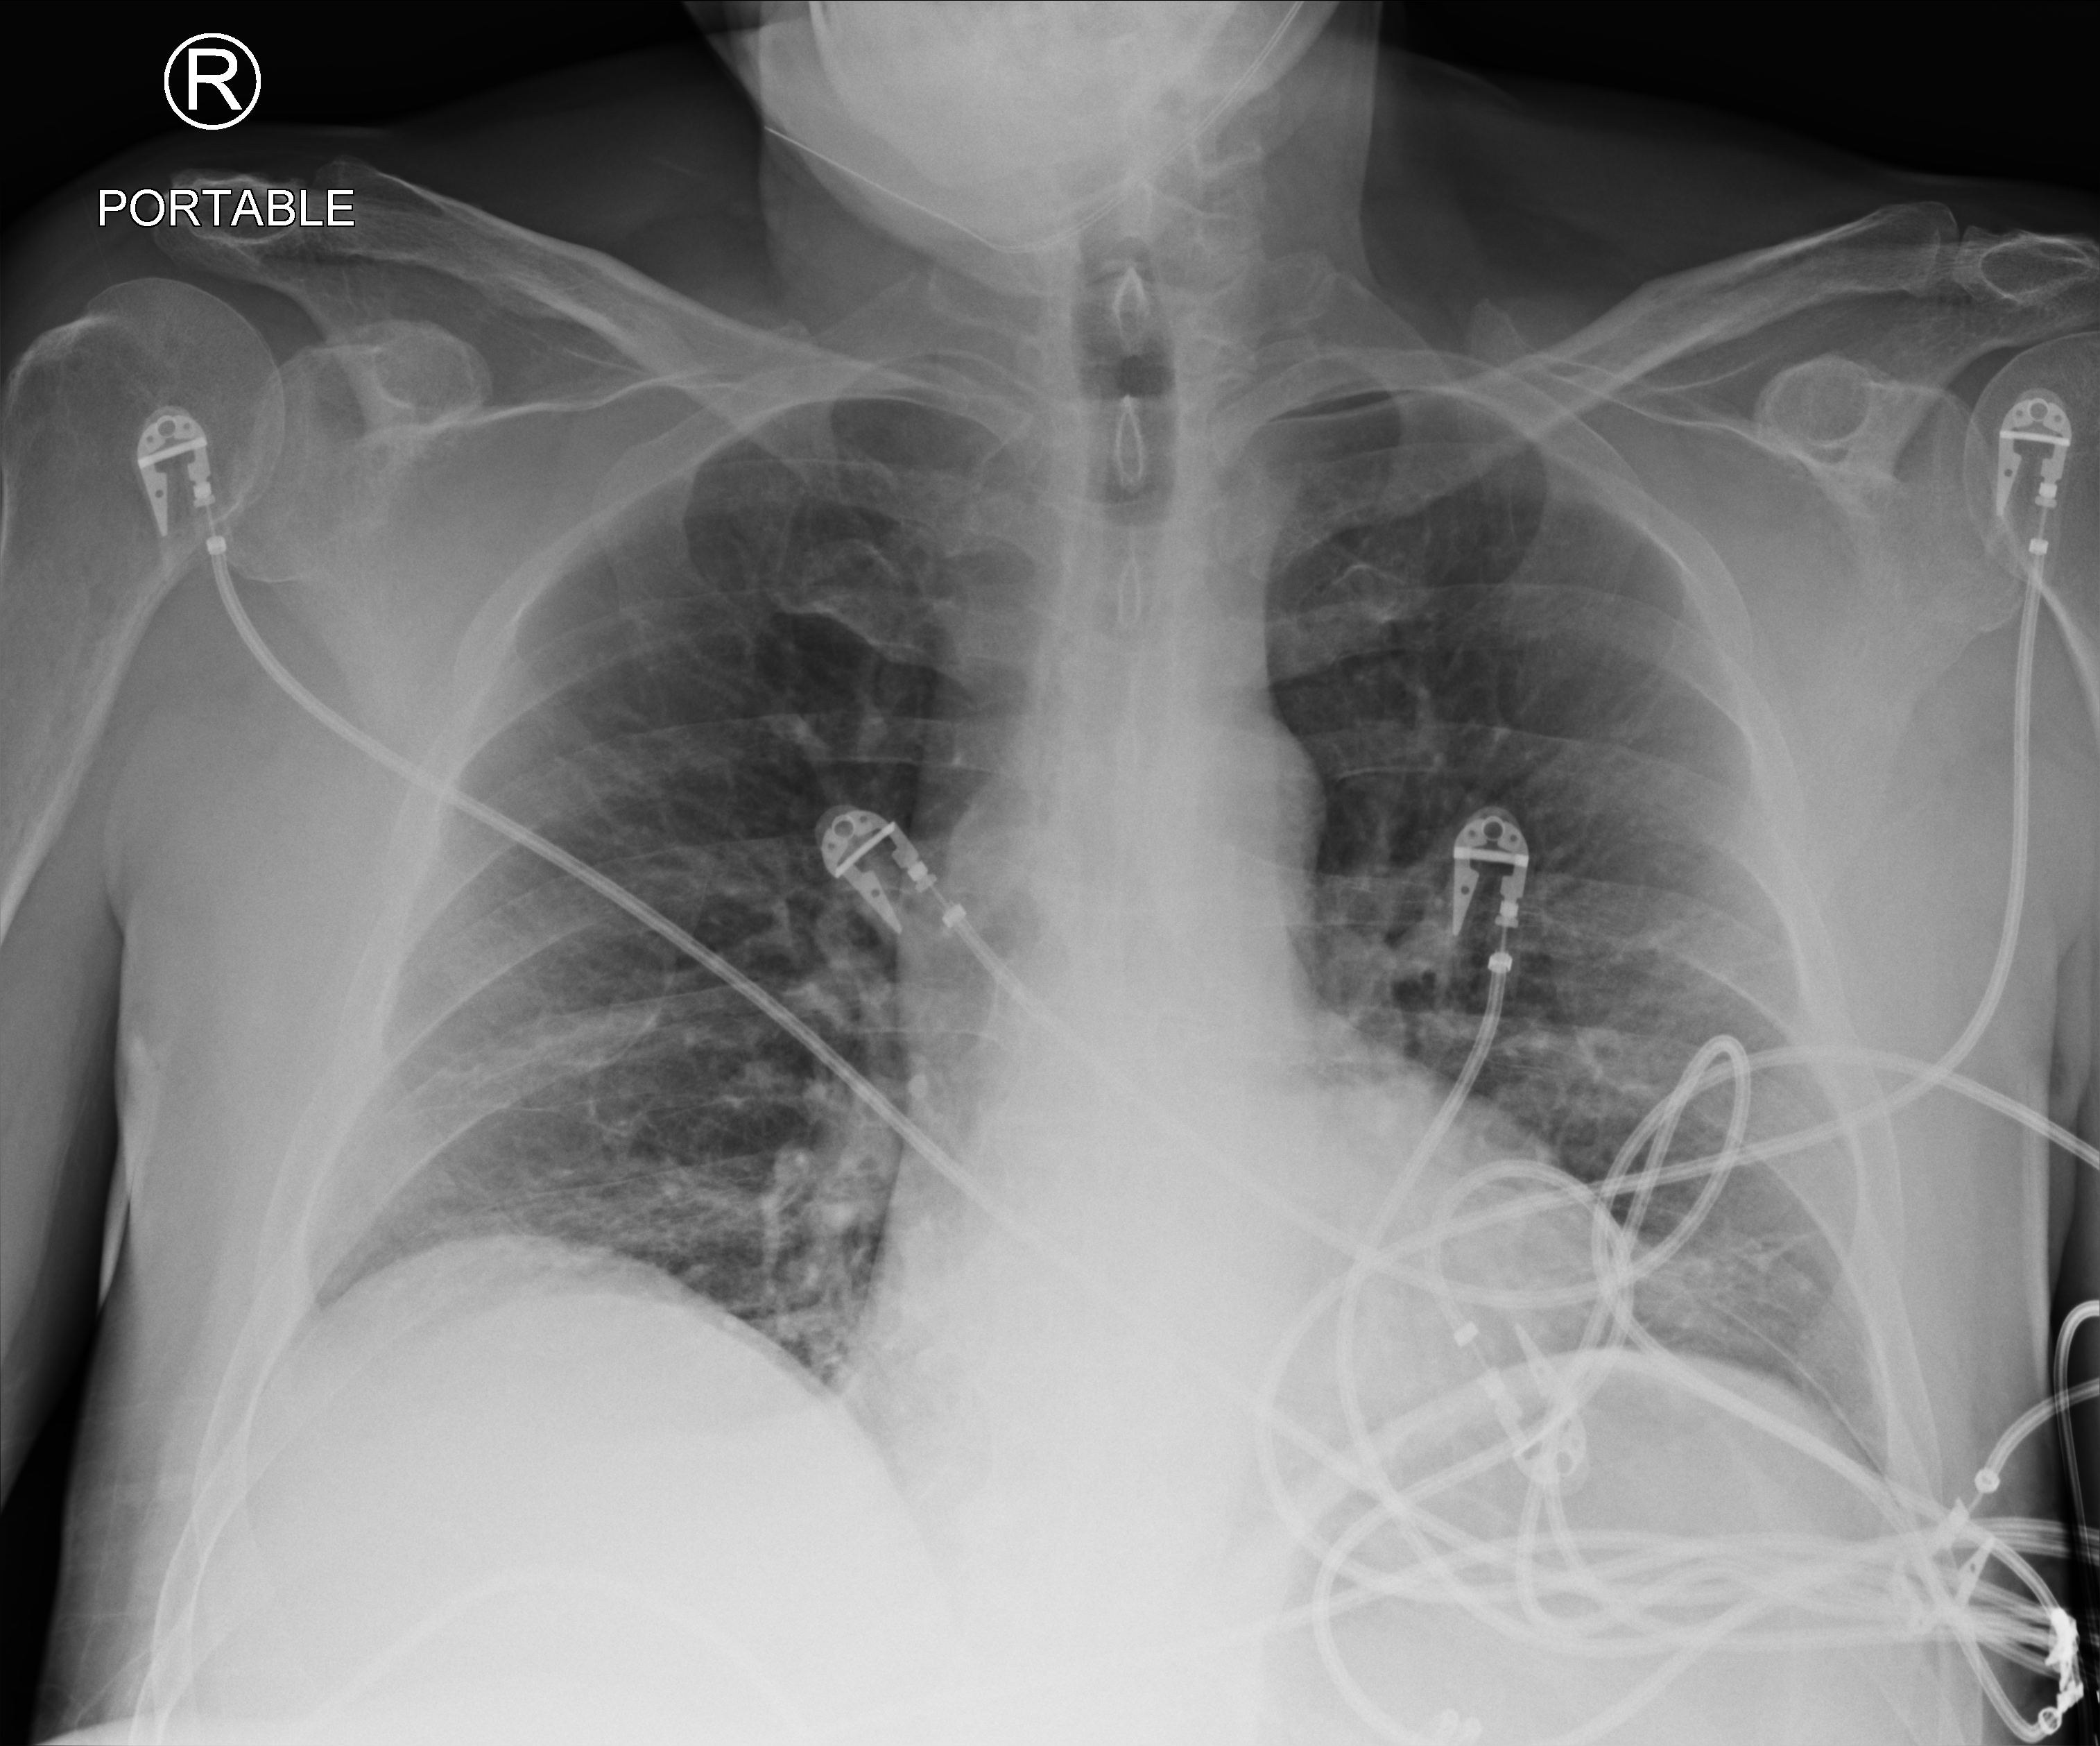
Portable chest radiograph; anteroposterior (AP) projection. Male patient hospitalised with COVID-19, age 60–74 years.
From the hospital-stay record, not from the radiograph (when in the stay this image was taken is not recorded):
- admitted to intensive care during this hospital stay: yes